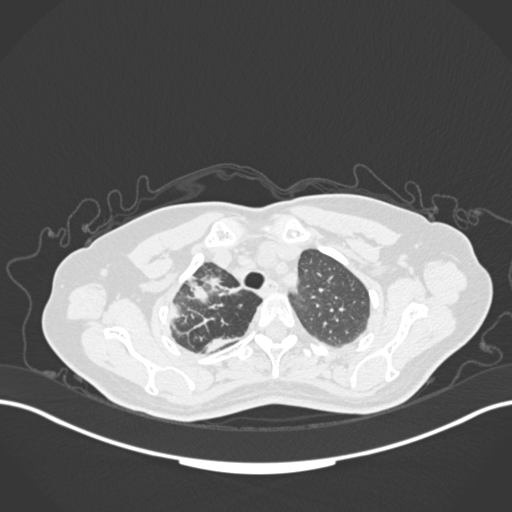
Chest CT, one axial slice. Slice 135 of 177 in the series (ordered by position). Lung window (W 1500 / L -600 HU). 1 mm slice thickness. 512 × 512 image matrix. Patient: female, 60 years. From the clinical record (not read from this slice): clinical TNM (as recorded): T3 N1 M1.
Annotated regions visible in this slice (rectangle marked by the reading radiologist):
- lung tumour (recorded histology: adenocarcinoma): bounding box [x1, y1, x2, y2] px = [158, 262, 240, 324]